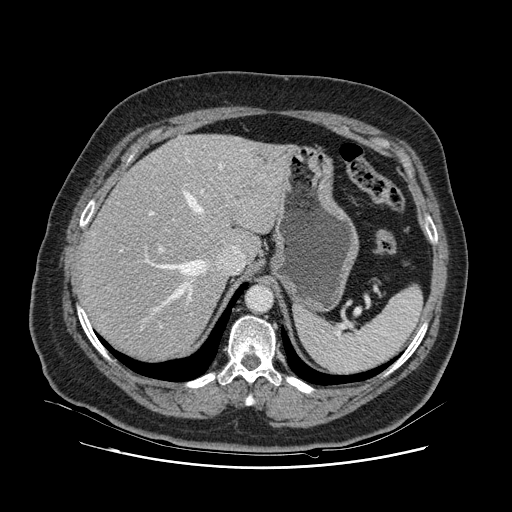
Contrast-enhanced abdominal CT, one axial slice; position 87 of 132 along the scan axis; intravenous contrast given; soft-tissue window (W 400 / L 40 HU); 512 × 512 image matrix, field of view 391 × 391 mm. Female patient, age 73 years. Case-level facts recorded for this patient, not image findings: diagnosis: colorectal cancer liver metastases, imaged before liver resection; multiple liver metastases: no; largest metastasis: 7 cm.
Annotated regions visible in this slice (expert manual segmentation):
- hepatic veins: bounding box [x1, y1, x2, y2] px = [140, 164, 235, 331]
- liver: [82, 135, 289, 360]
- planned liver remnant (the part of the liver to remain after resection): [82, 161, 247, 360]
- portal vein (with intrahepatic branches): [120, 159, 190, 327]